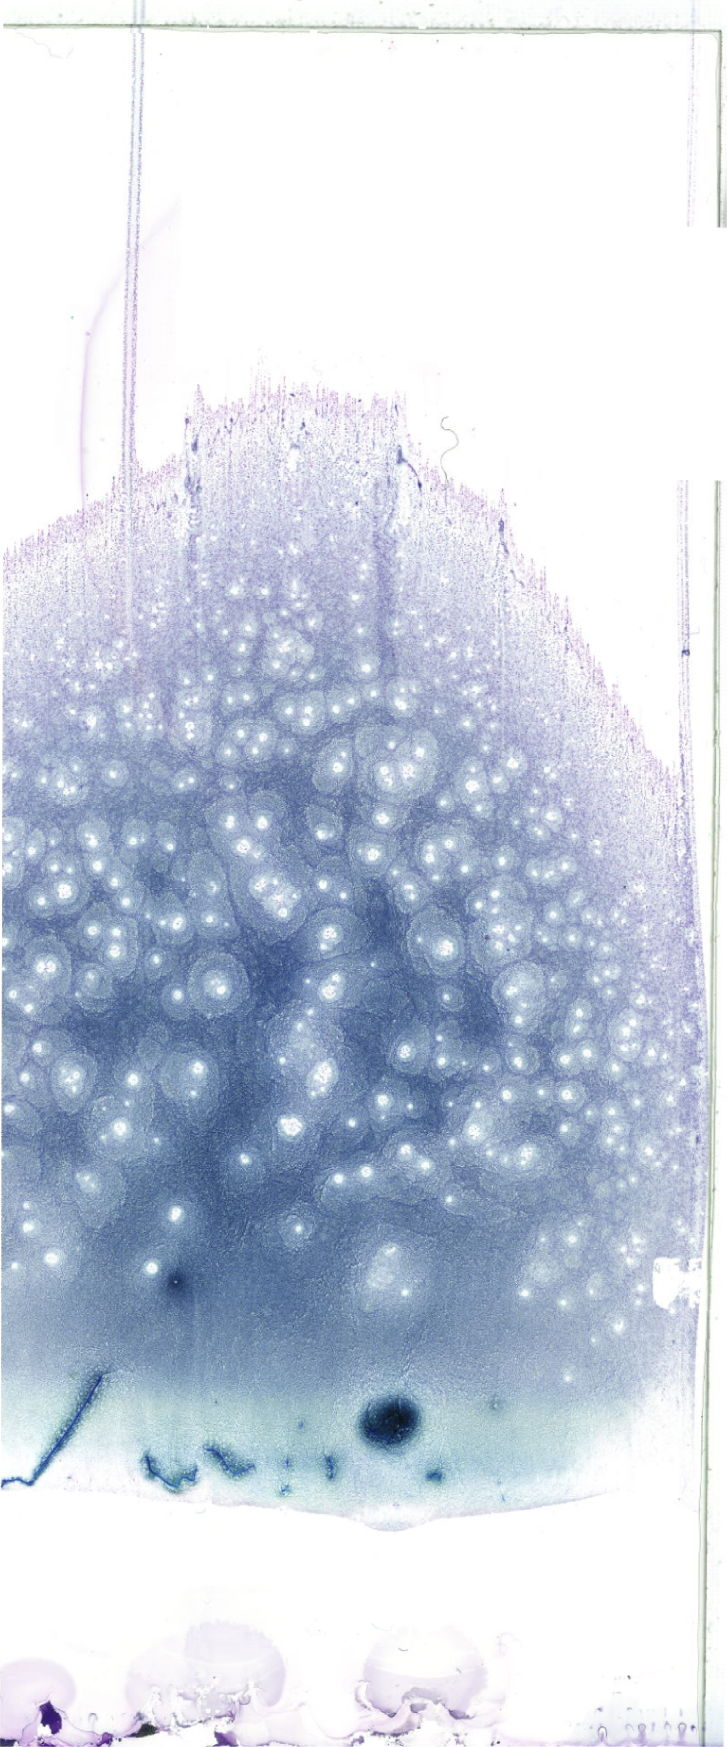
Whole-slide image of a May-Grünwald-Giemsa (MGG)-stained bone marrow aspirate smear, whole scanned area (about 20.6 x 49.5 mm) shown as a low-resolution overview. Patient sex: female.
Diagnosis: Mixed Phenotype Acute Leukemia, B/Myeloid.